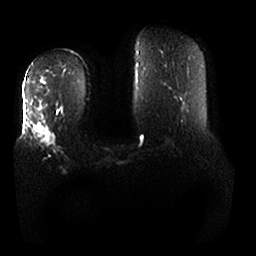
Breast MRI, one axial slice; position 9 of 25 along the scan axis; diffusion-weighted series; image 2 of 4 stored at this slice position (different b-values; order by instance number); 1.5 T; 4 mm slice thickness; 256 × 256 image matrix, field of view 380 × 380 mm. Female patient.
Outlined on this slice (manually delineated by an expert):
- tumour on diffusion-weighted imaging: bounding box [x1, y1, x2, y2] px = [34, 124, 54, 145]